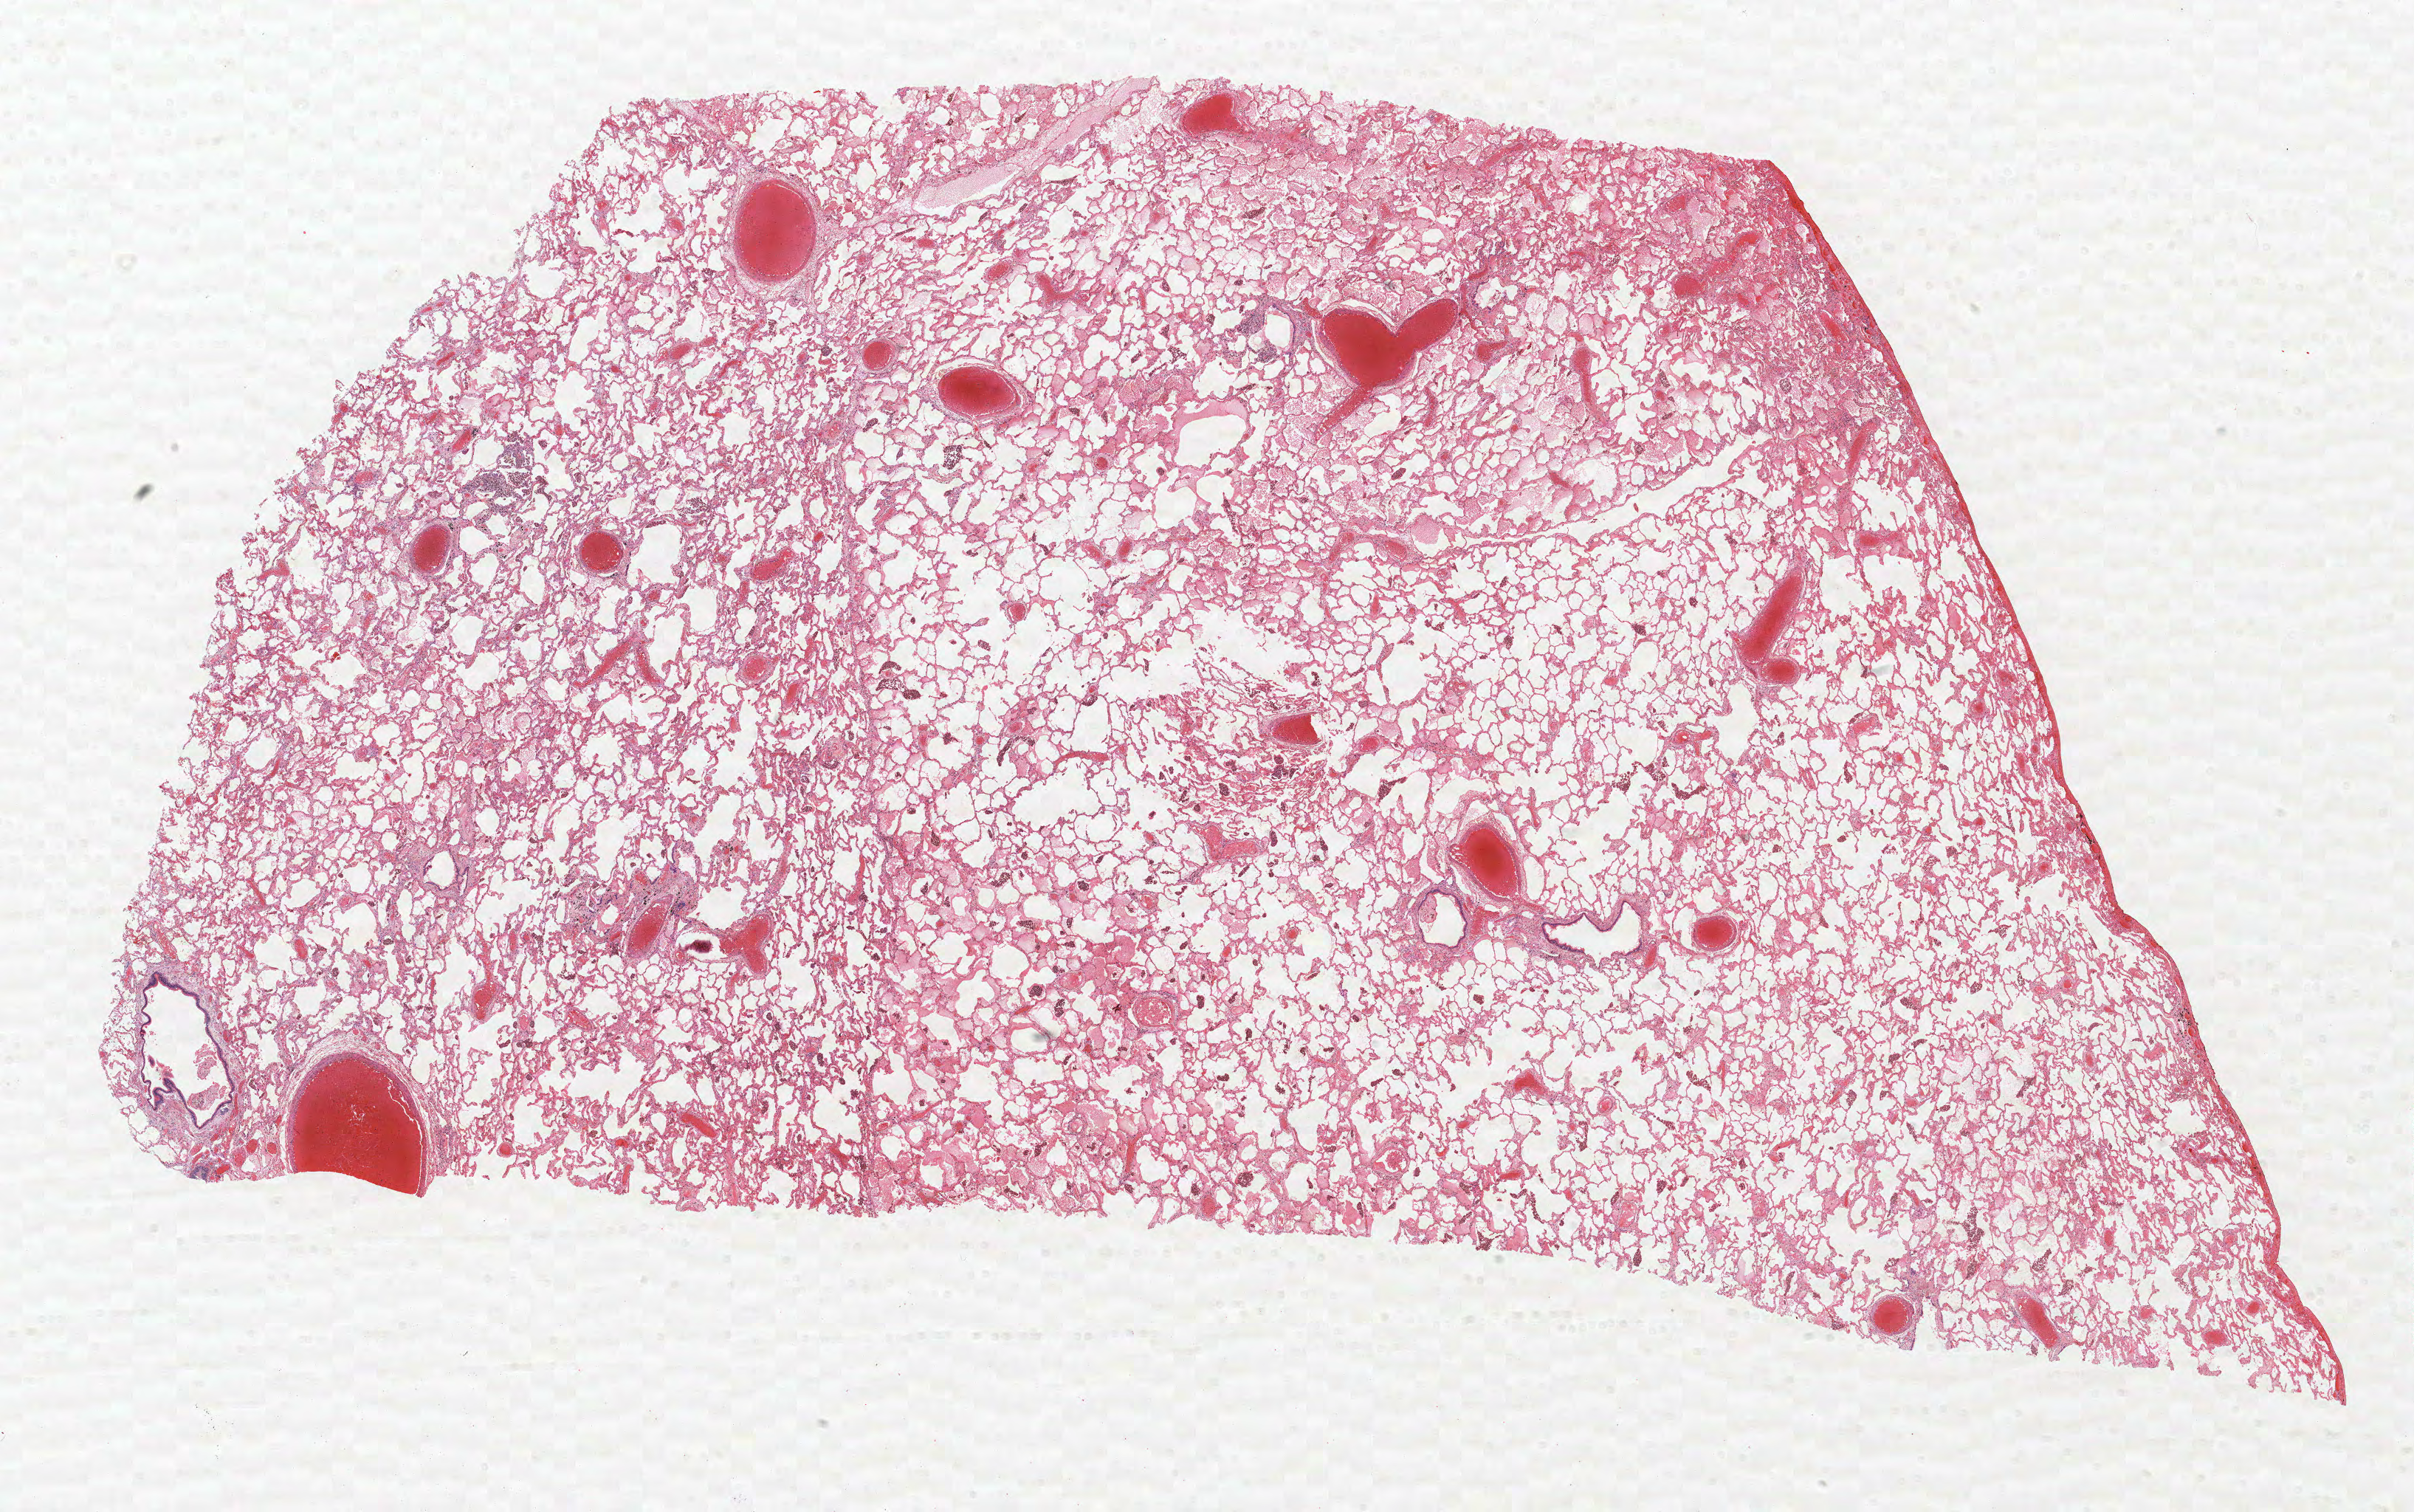
Whole-slide histology image, Hematoxylin and eosin (H&E) stained, low-resolution overview of the scanned area, about 26.2 x 16.4 mm (slide scanned at 40x). Formalin-fixed paraffin-embedded (FFPE) section. Lung. Female patient, aged 57 at enrolment. Grade: poorly differentiated (G3).
Participant's lung-cancer diagnosis: Adenosquamous carcinoma. Stage (AJCC 6th edition): IIIA. ICD-O-3 topography: upper lobe of lung (C34.1). Tumour size (pathology): 60 mm. Primary tumour location (clinical record): right upper lobe.